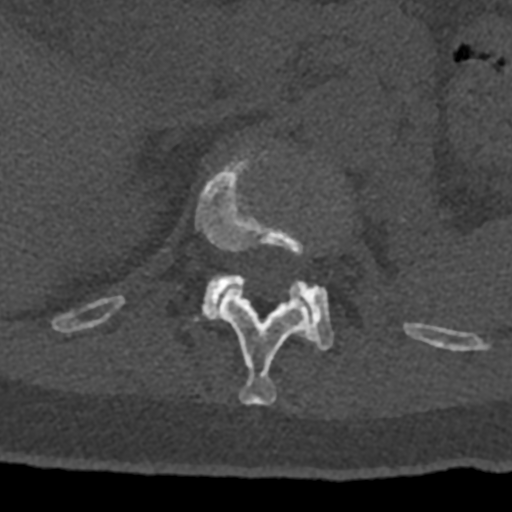
CT including the spine, one axial slice. Position 471 of 797 along the scan axis. Reconstruction kernel Br40s/3. 120 kVp. Bone window (W 1800 / L 400 HU). 0.5 mm slice thickness. 512 × 512 image matrix. Male patient, age 74 years. Case-level facts recorded for this patient, not image findings: primary cancer: renal; vertebrae with lytic lesions (as recorded): T10, L1, L2, L3, L4, L5.
Outlined on this slice (semi-automatic segmentation, software-assisted and operator-edited):
- L1 vertebra: bounding box (x1, y1, x2, y2) in pixels: (194, 274, 334, 351)
- T12 vertebra: (70, 154, 432, 405)